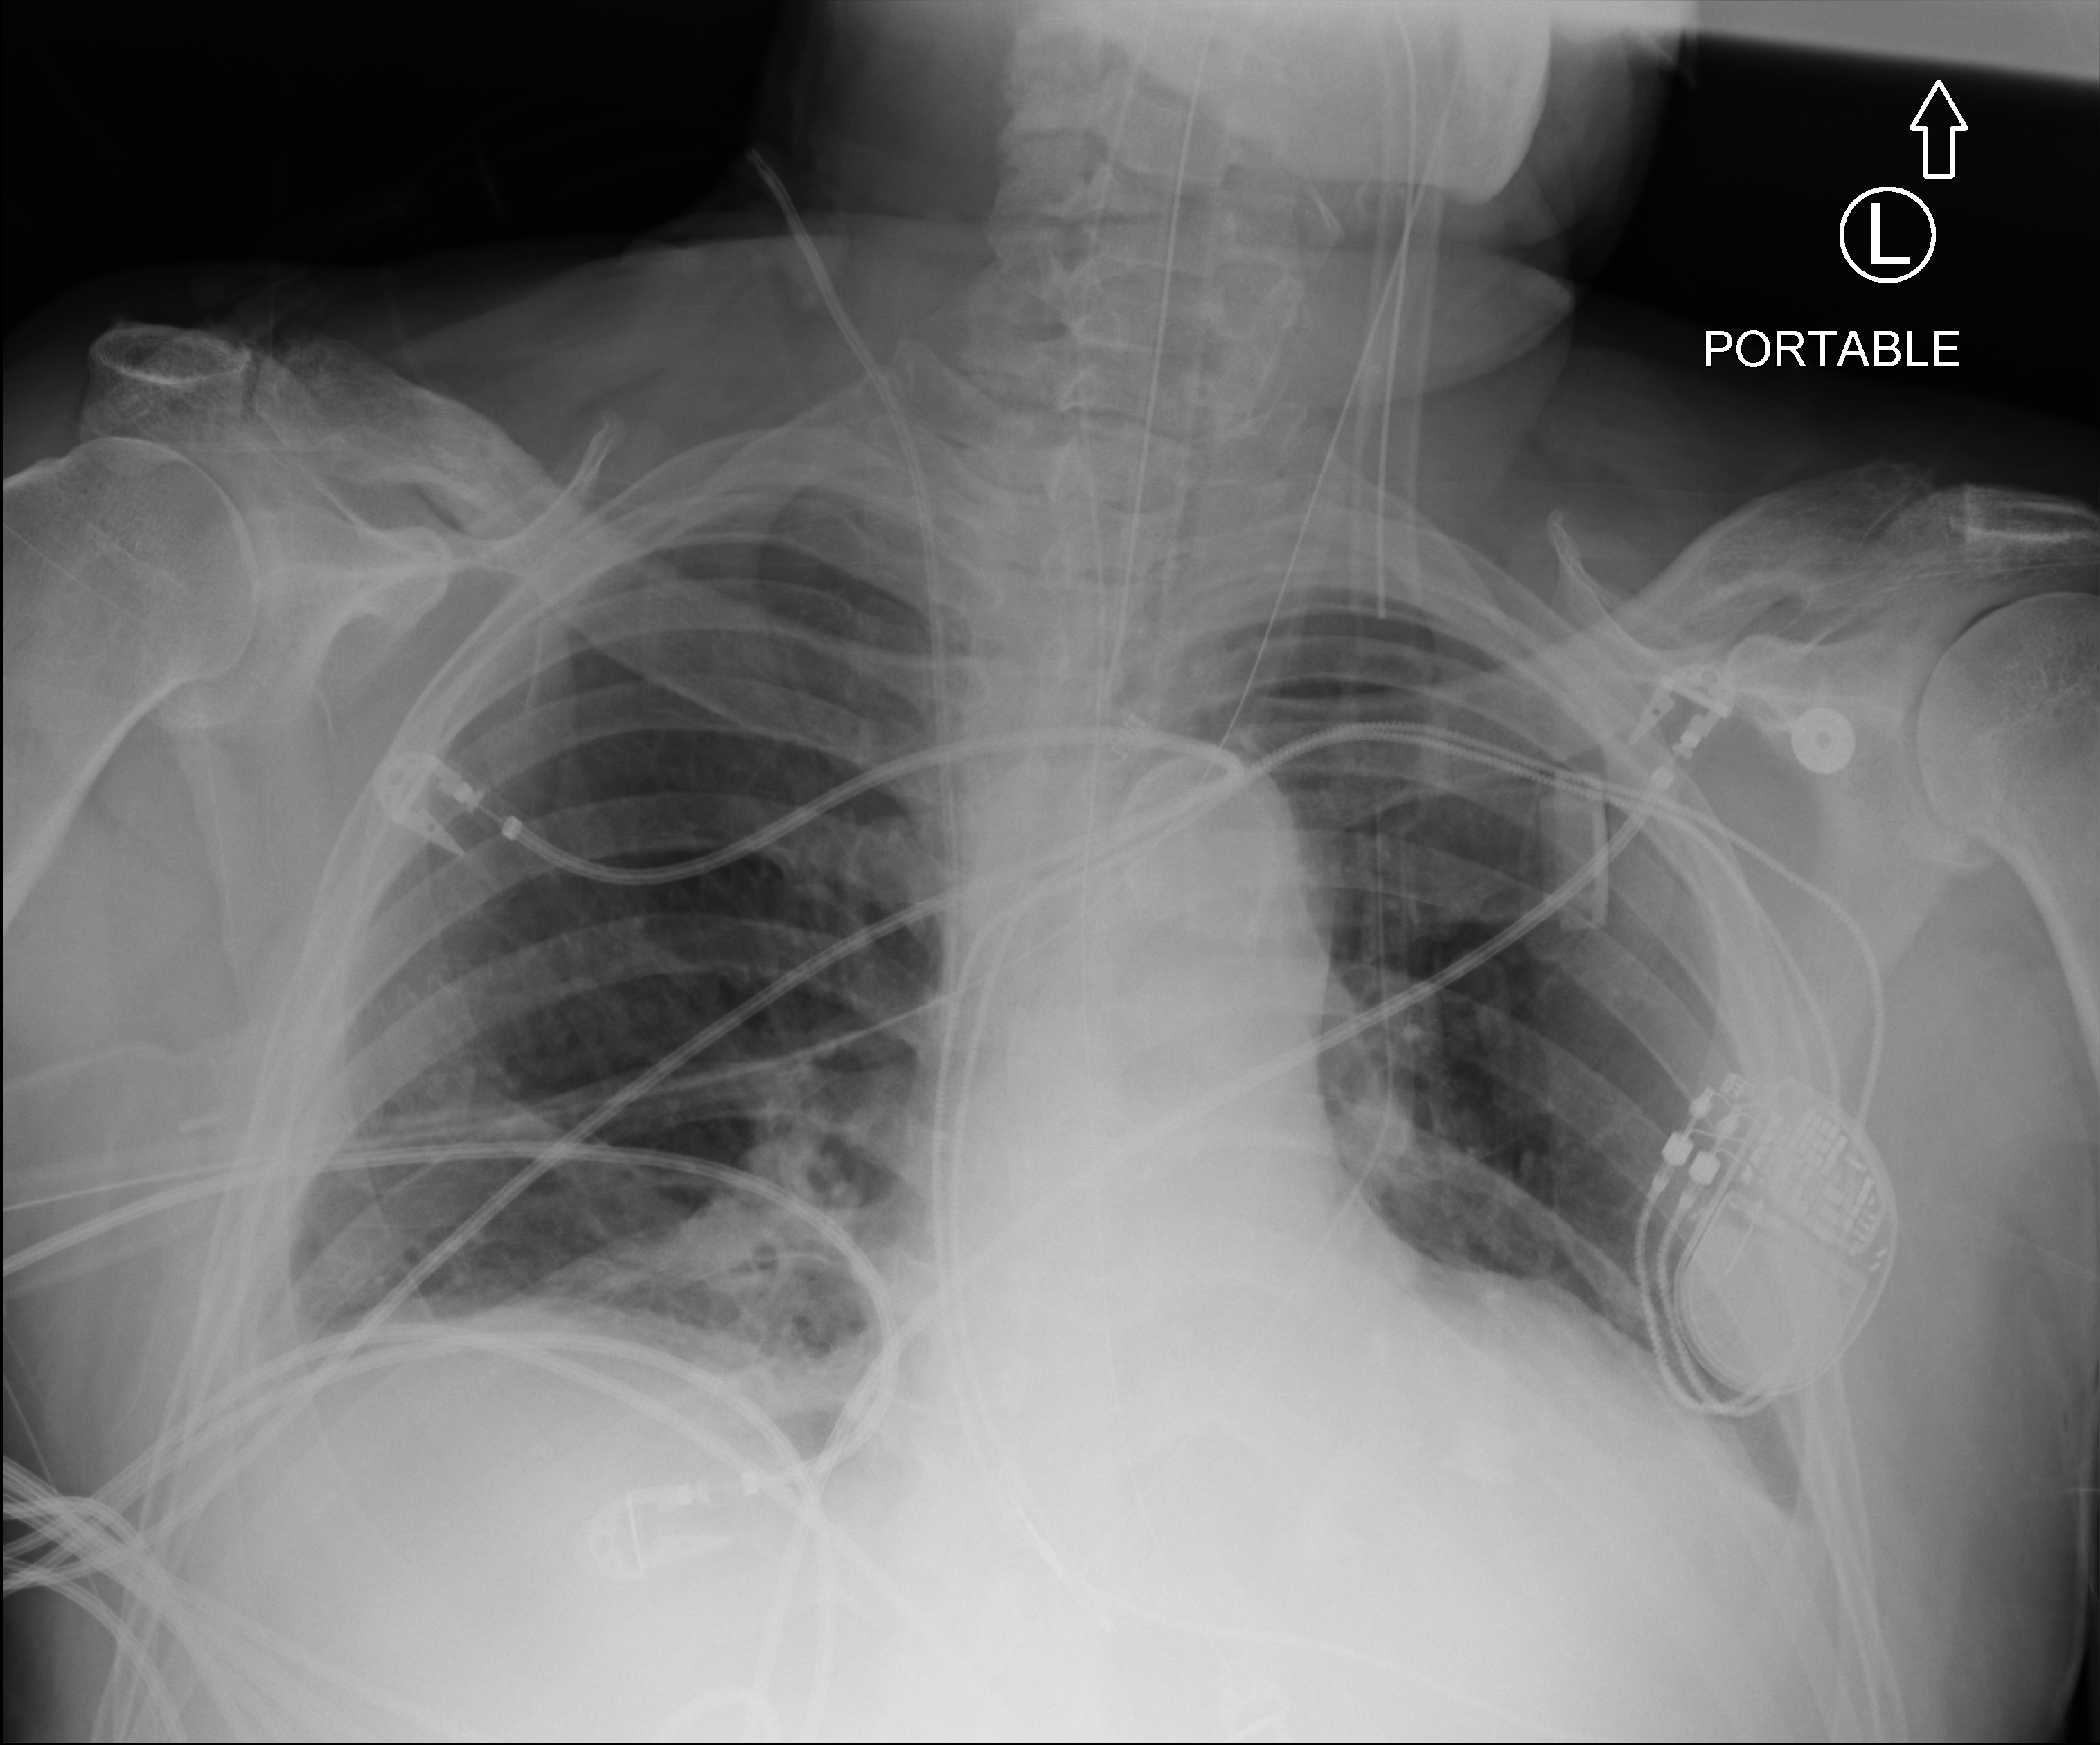
Chest X-ray (portable); anteroposterior (AP) projection. Patient hospitalised with COVID-19; male, aged 60–74 years.
From the hospital-stay record, not from the radiograph (when in the stay this image was taken is not recorded): admitted to intensive care during this hospital stay: yes; mechanically ventilated during this hospital stay: yes.